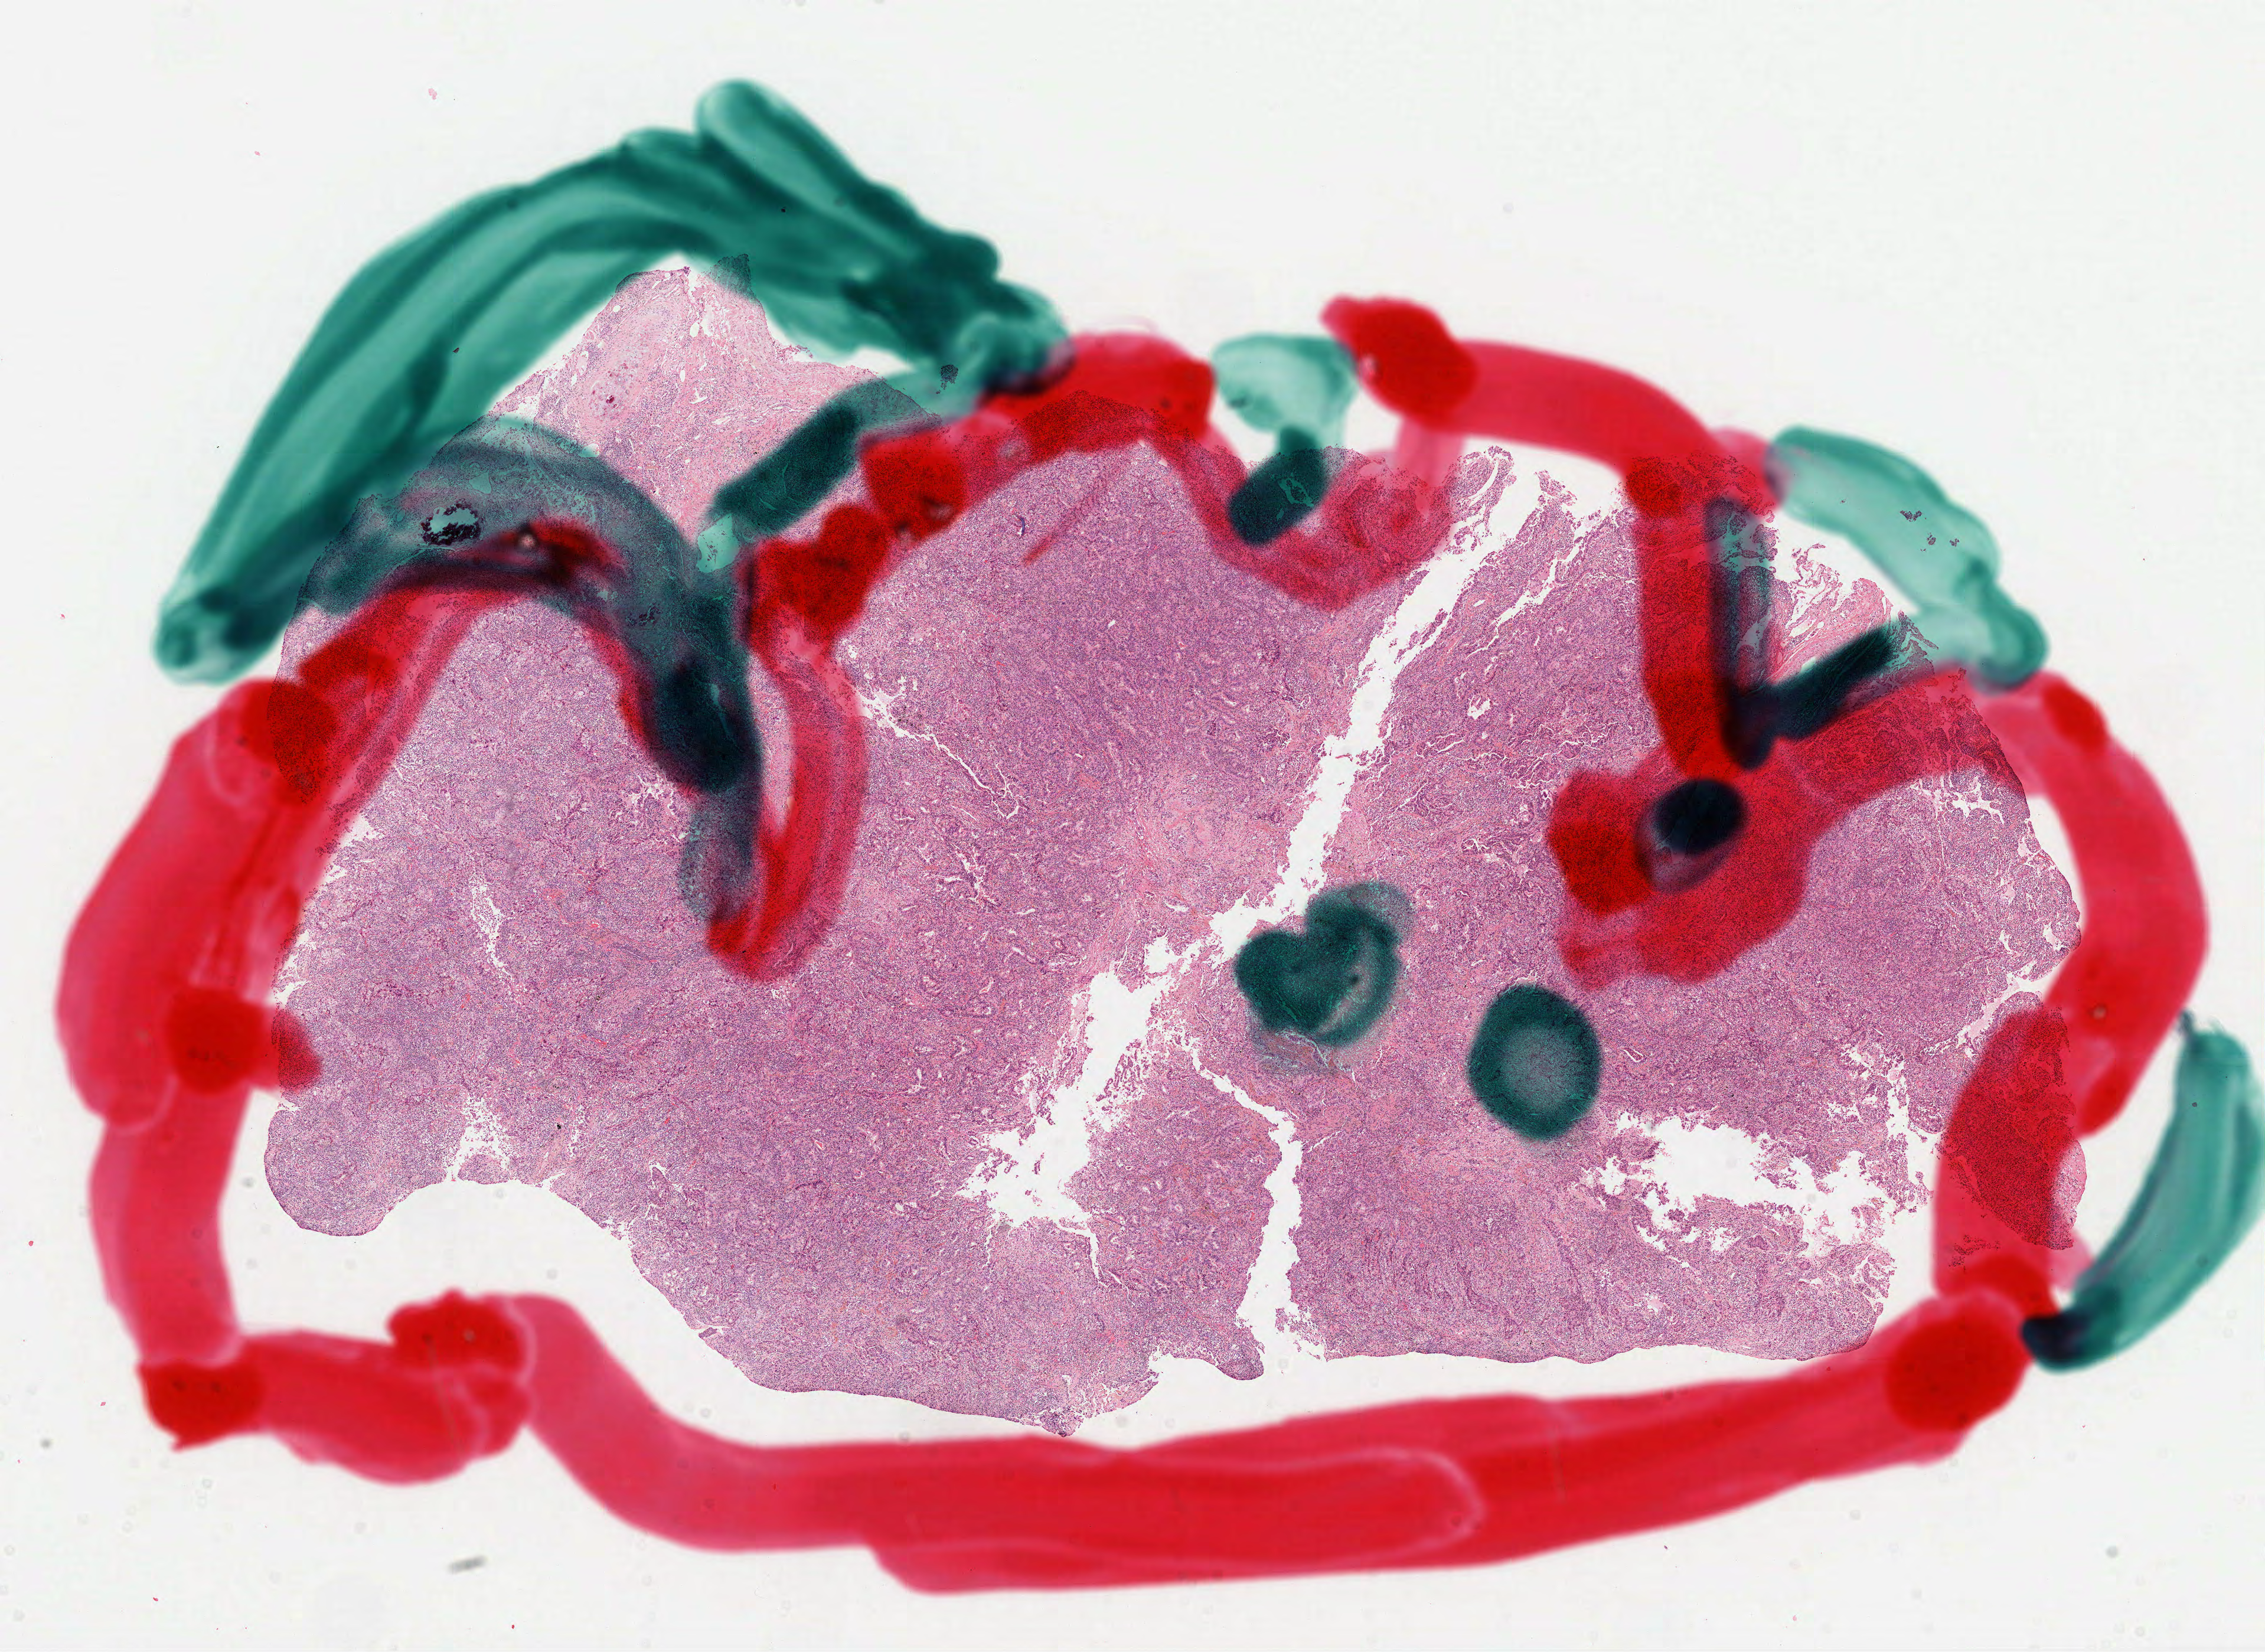
Whole-slide histology image, Hematoxylin and eosin (H&E) stained, shown as a low-resolution overview of the whole scanned area (about 15.5 x 11.3 mm, acquisition: 40x scan); formalin-fixed paraffin-embedded (FFPE) diagnostic section; lung, primary tumour sample. Female, age 73 years at initial diagnosis.
Pathologic diagnosis: Adenocarcinoma with mixed subtypes (upper lobe, lung).